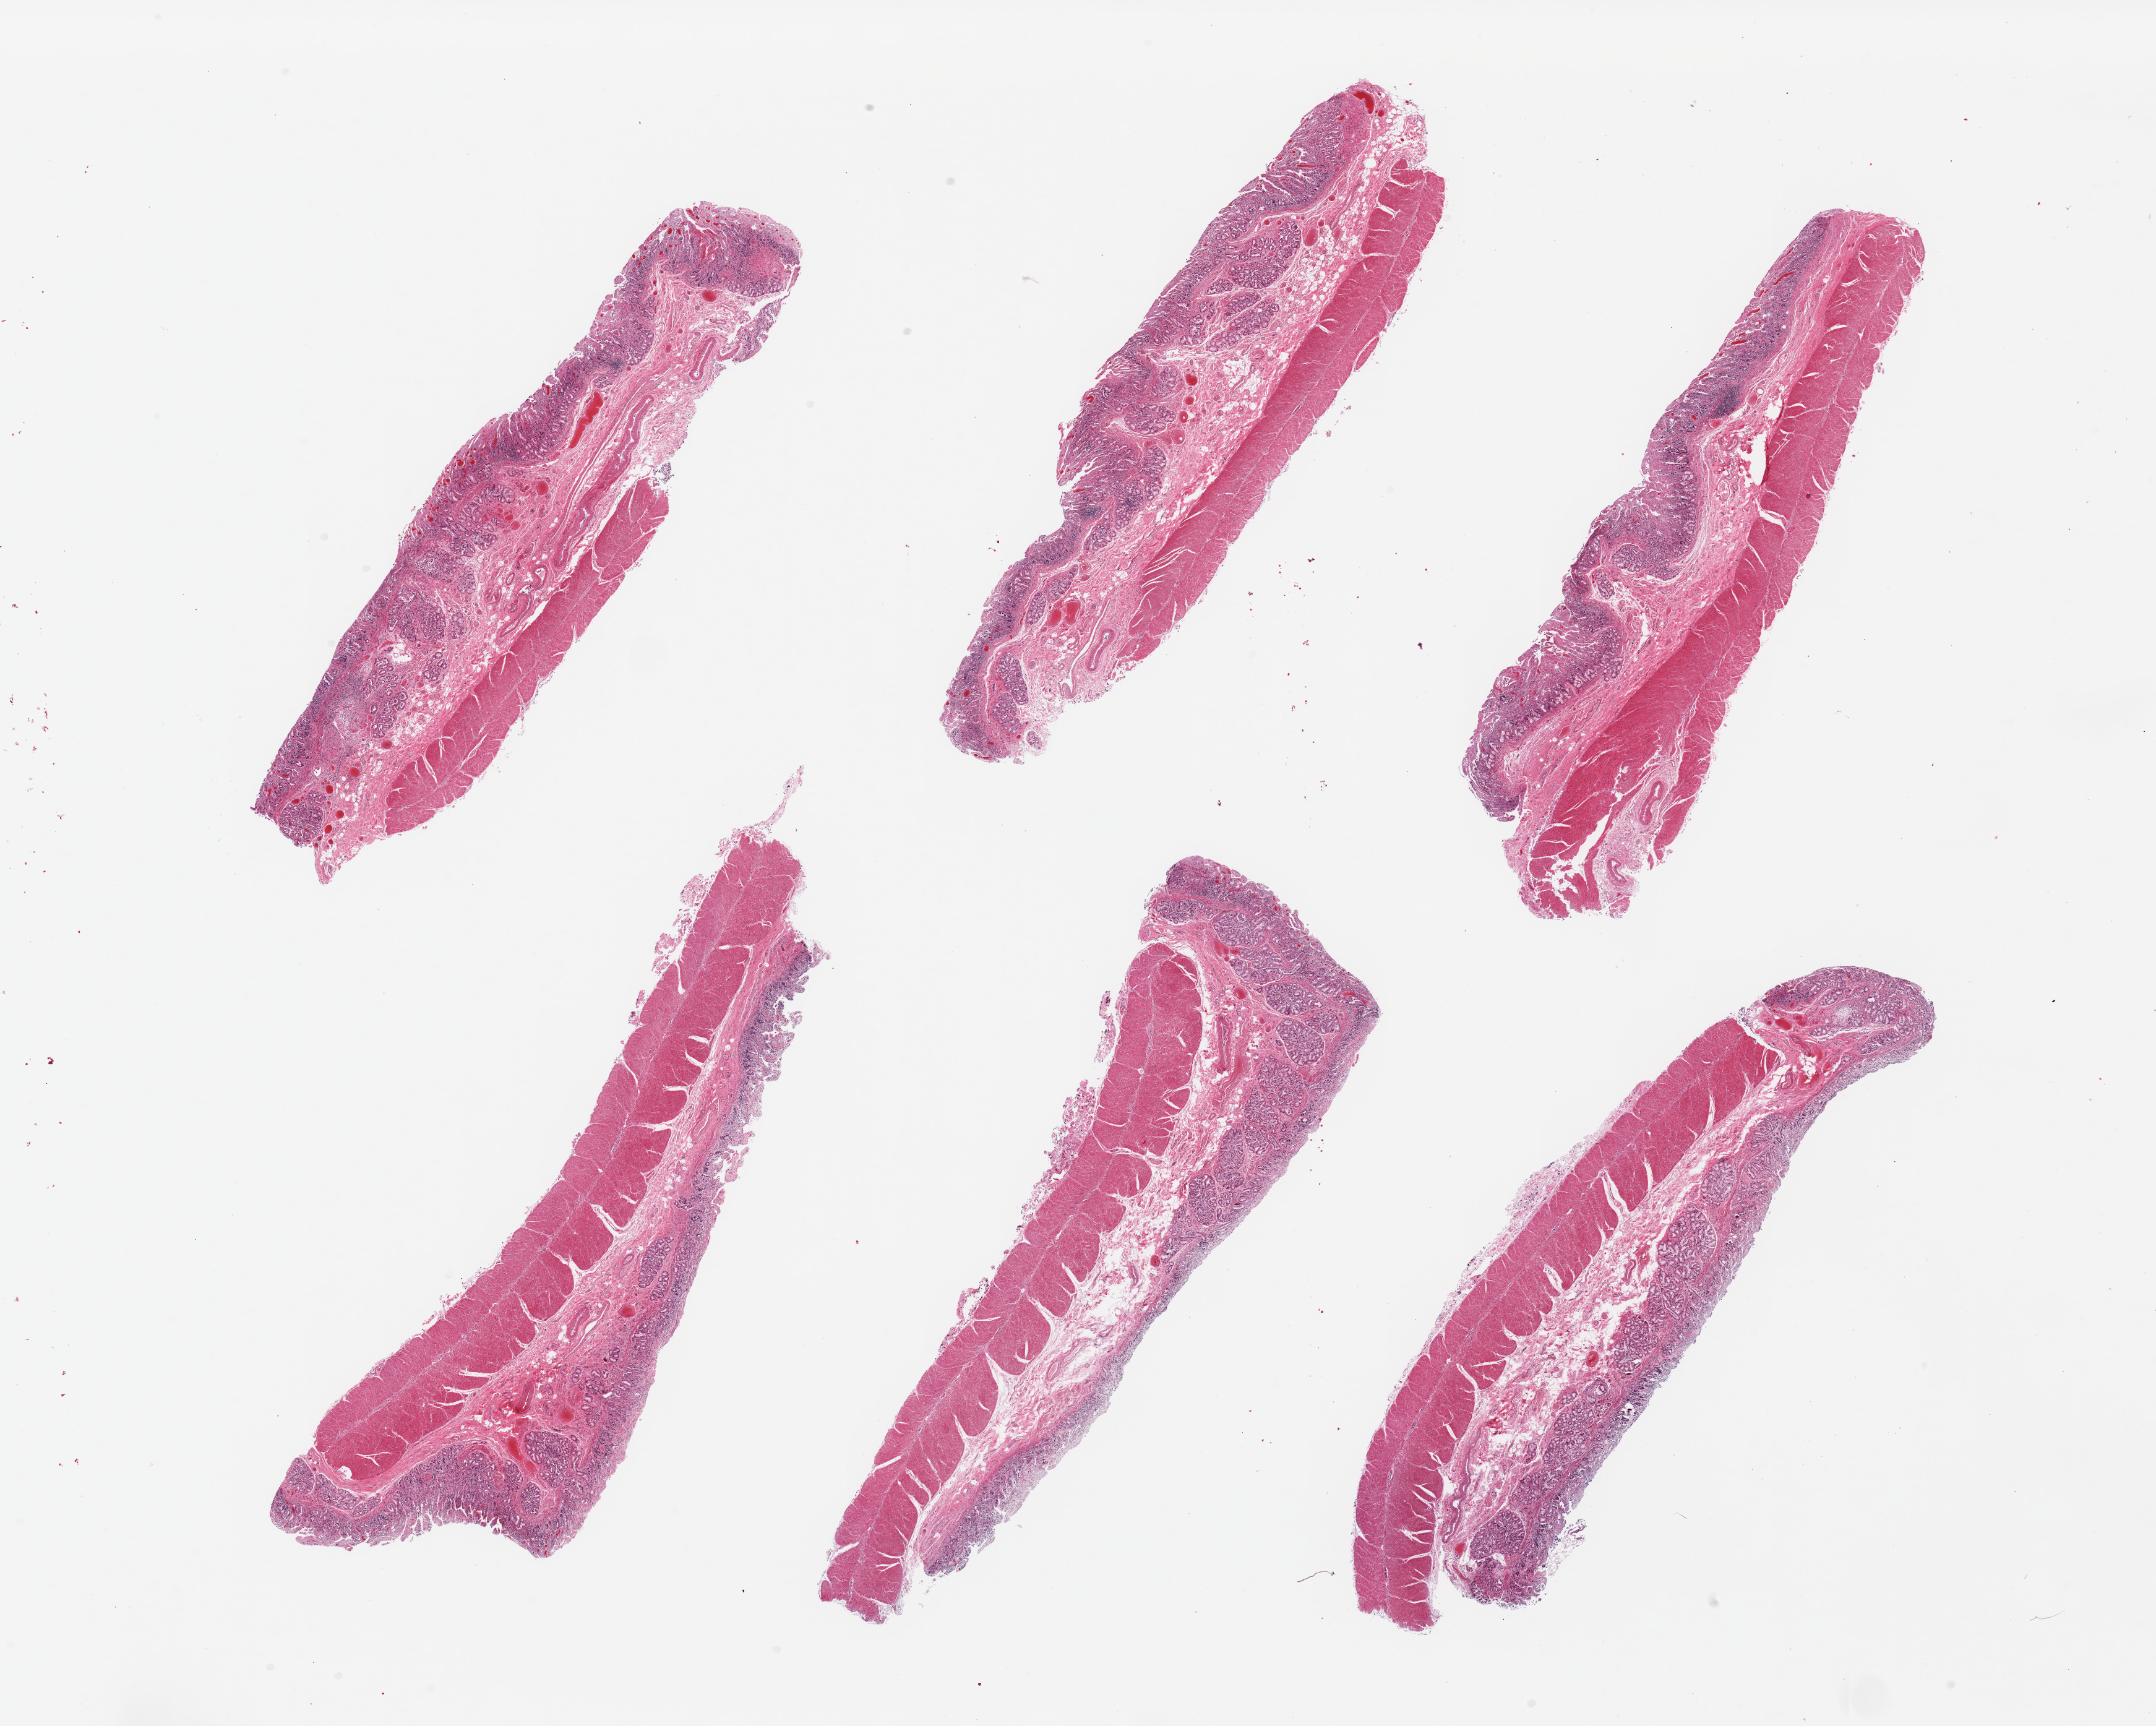
Haematoxylin and eosin whole-slide image — a low-resolution overview of the entire scanned area, about 27.6 x 22.1 mm; PAXgene-fixed paraffin-embedded (PFPE) section; section of ileum (target tissue); tissue donor sample. Donor: male.
* reviewer comment on this tissue sample: 6 pieces, autolyzed mucosa, no target lymphoid aggregates